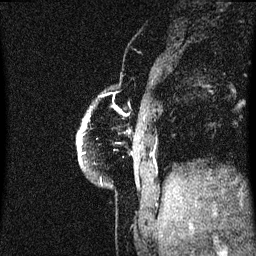
Breast MRI (dynamic contrast-enhanced), one sagittal slice. Slice 7 of 60 in the series (ordered by position). Dynamic contrast-enhanced series, image 2 of 3 at this slice position (ordered by acquisition). 1.5 T. TE 4.2 ms, TR 8.4 ms. 2 mm slice thickness. 256 × 256 image matrix. Patient: female, 60 years.
Outlined on this slice (semi-automatically segmented with operator editing):
- analysis volume of interest (the breast-tissue region the enhancement analysis was run in; not a lesion): box from (x=78, y=104) to (x=101, y=181) px
- tumour enhancement mask (voxels above the 70 % enhancement threshold inside the analysis volume of interest): (x=78, y=126)–(x=85, y=159)